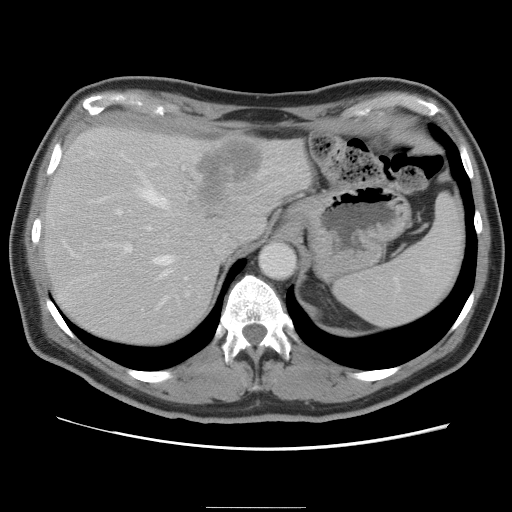
Contrast-enhanced abdominal CT, one axial slice. Slice 61 of 87 in the series (ordered by position). 120 kVp. Intravenous contrast given. Soft-tissue window (W 400 / L 40 HU). 5 mm slice thickness. 512 × 512 image matrix, field of view 363 × 363 mm. Male patient, age 63 years. Case-level facts recorded for this patient, not image findings: diagnosis: colorectal cancer liver metastases, imaged before liver resection; multiple liver metastases: no; largest metastasis: 9 cm.
Outlined on this slice (outlined manually by an expert reader):
- hepatic veins: box from (x=96, y=159) to (x=187, y=306) px
- liver: (x=43, y=126)–(x=312, y=347)
- planned liver remnant (the part of the liver to remain after resection): (x=43, y=157)–(x=220, y=347)
- portal vein (with intrahepatic branches): (x=104, y=208)–(x=189, y=296)
- liver metastasis: (x=199, y=140)–(x=262, y=205)